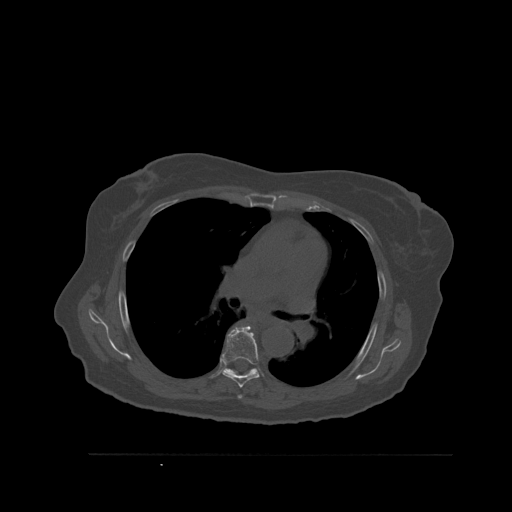
CT including the spine, one axial slice; position 378 of 527 along the scan axis; bone window (W 1800 / L 400 HU); 1.5 mm slice thickness; 512 × 512 image matrix. Female patient, age 73 years. Case-level facts recorded for this patient, not image findings: primary cancer: breast.
Outlined on this slice (semi-automatic segmentation, software-assisted and operator-edited):
- T5 vertebra: bounding box <238,395,242,399> (left, top, right, bottom; pixels)
- T6 vertebra: <221,325,260,388>
- T7 vertebra: <225,368,257,376>